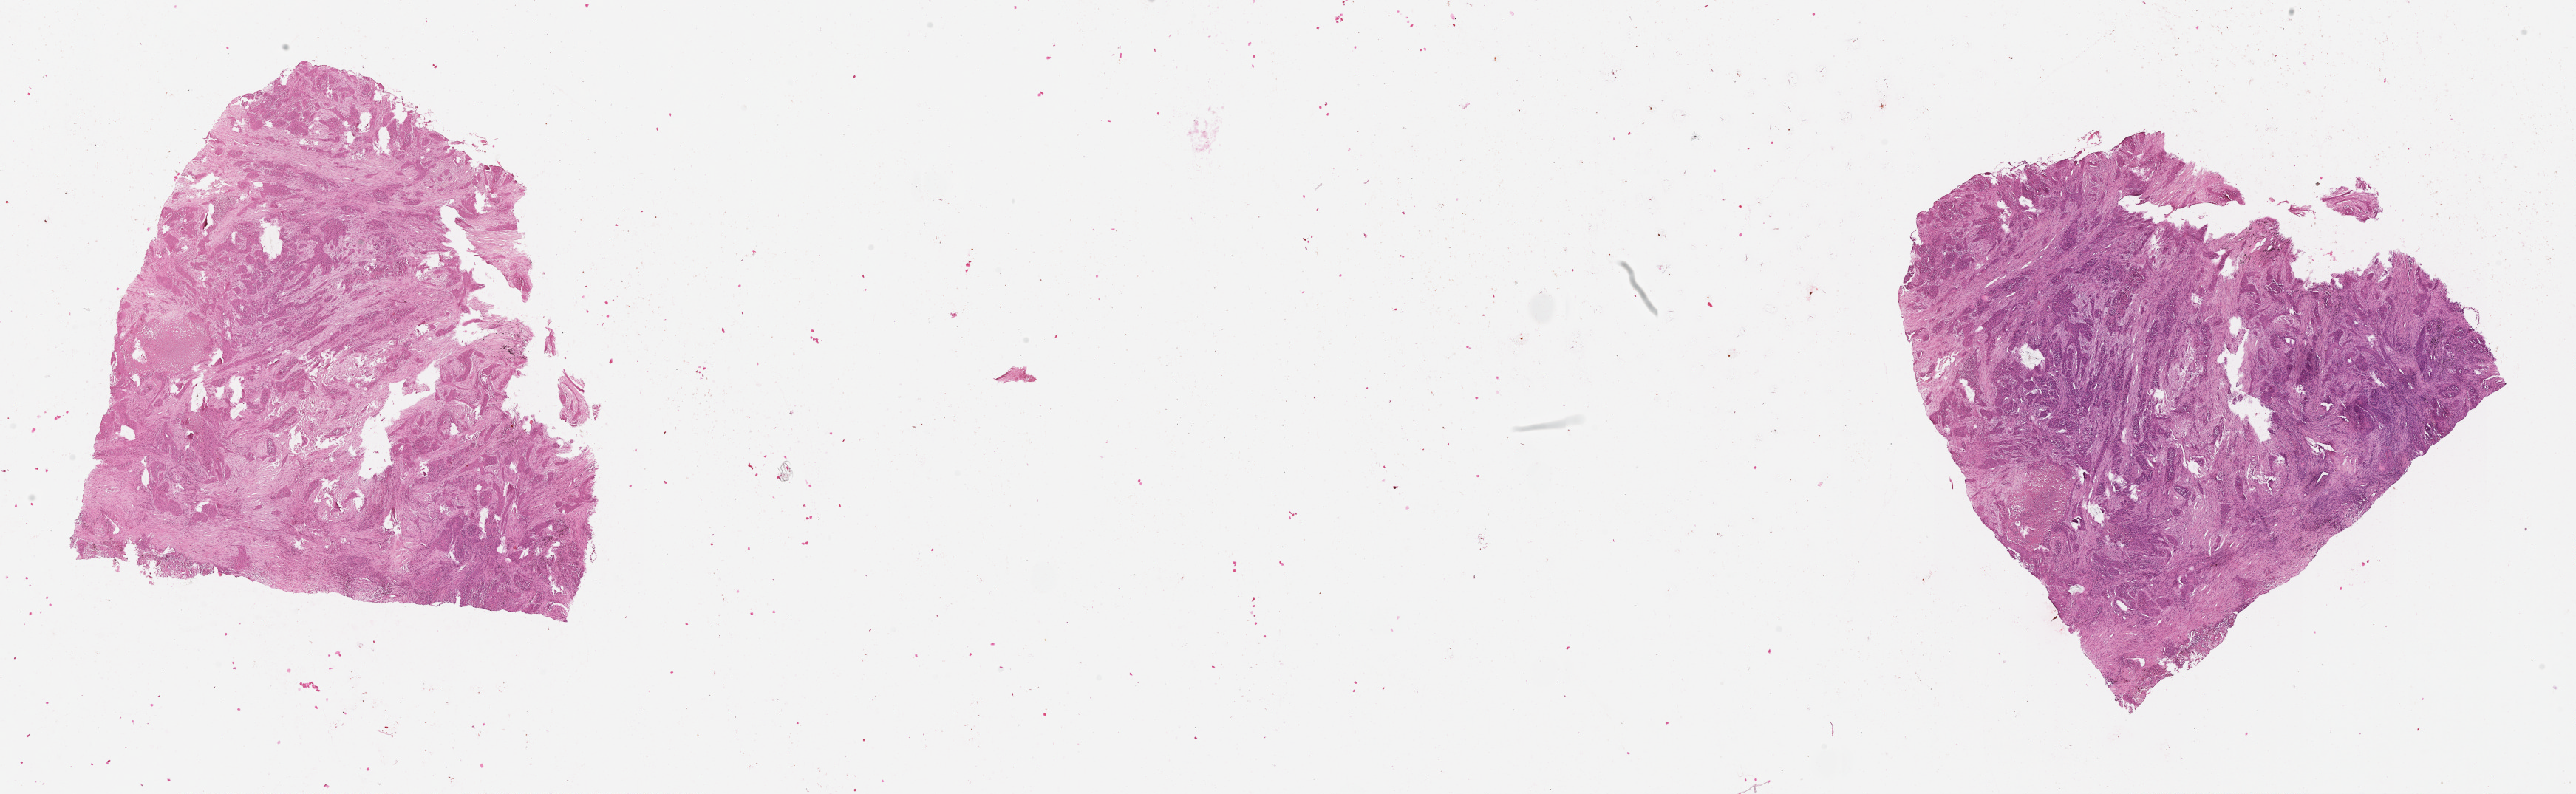
H&E whole-slide image, whole scanned area (about 28.1 x 8.7 mm, slide scanned at 20x) shown as a low-resolution overview, tumour tissue sample, lung. Male, 79 y/o.
Patient diagnosis (cohort enrolment): squamous cell carcinoma (lung).